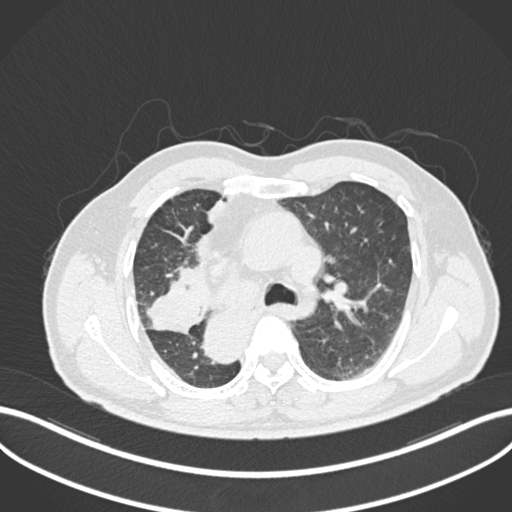
Chest CT, one axial slice; slice 157 of 206 in the series (ordered by position); reconstruction kernel B30f; 120 kVp; lung window (W 1500 / L -600 HU); 1 mm slice thickness; 512 × 512 image matrix. Male patient, age 67 years. Case-level facts recorded for this patient, not image findings: clinical TNM (as recorded): T2a N0 M0.
Structures marked on this image (rectangle marked by the reading radiologist):
- lung tumour (recorded histology: squamous cell carcinoma): bounding box (x1, y1, x2, y2) in pixels: (143, 277, 203, 336)